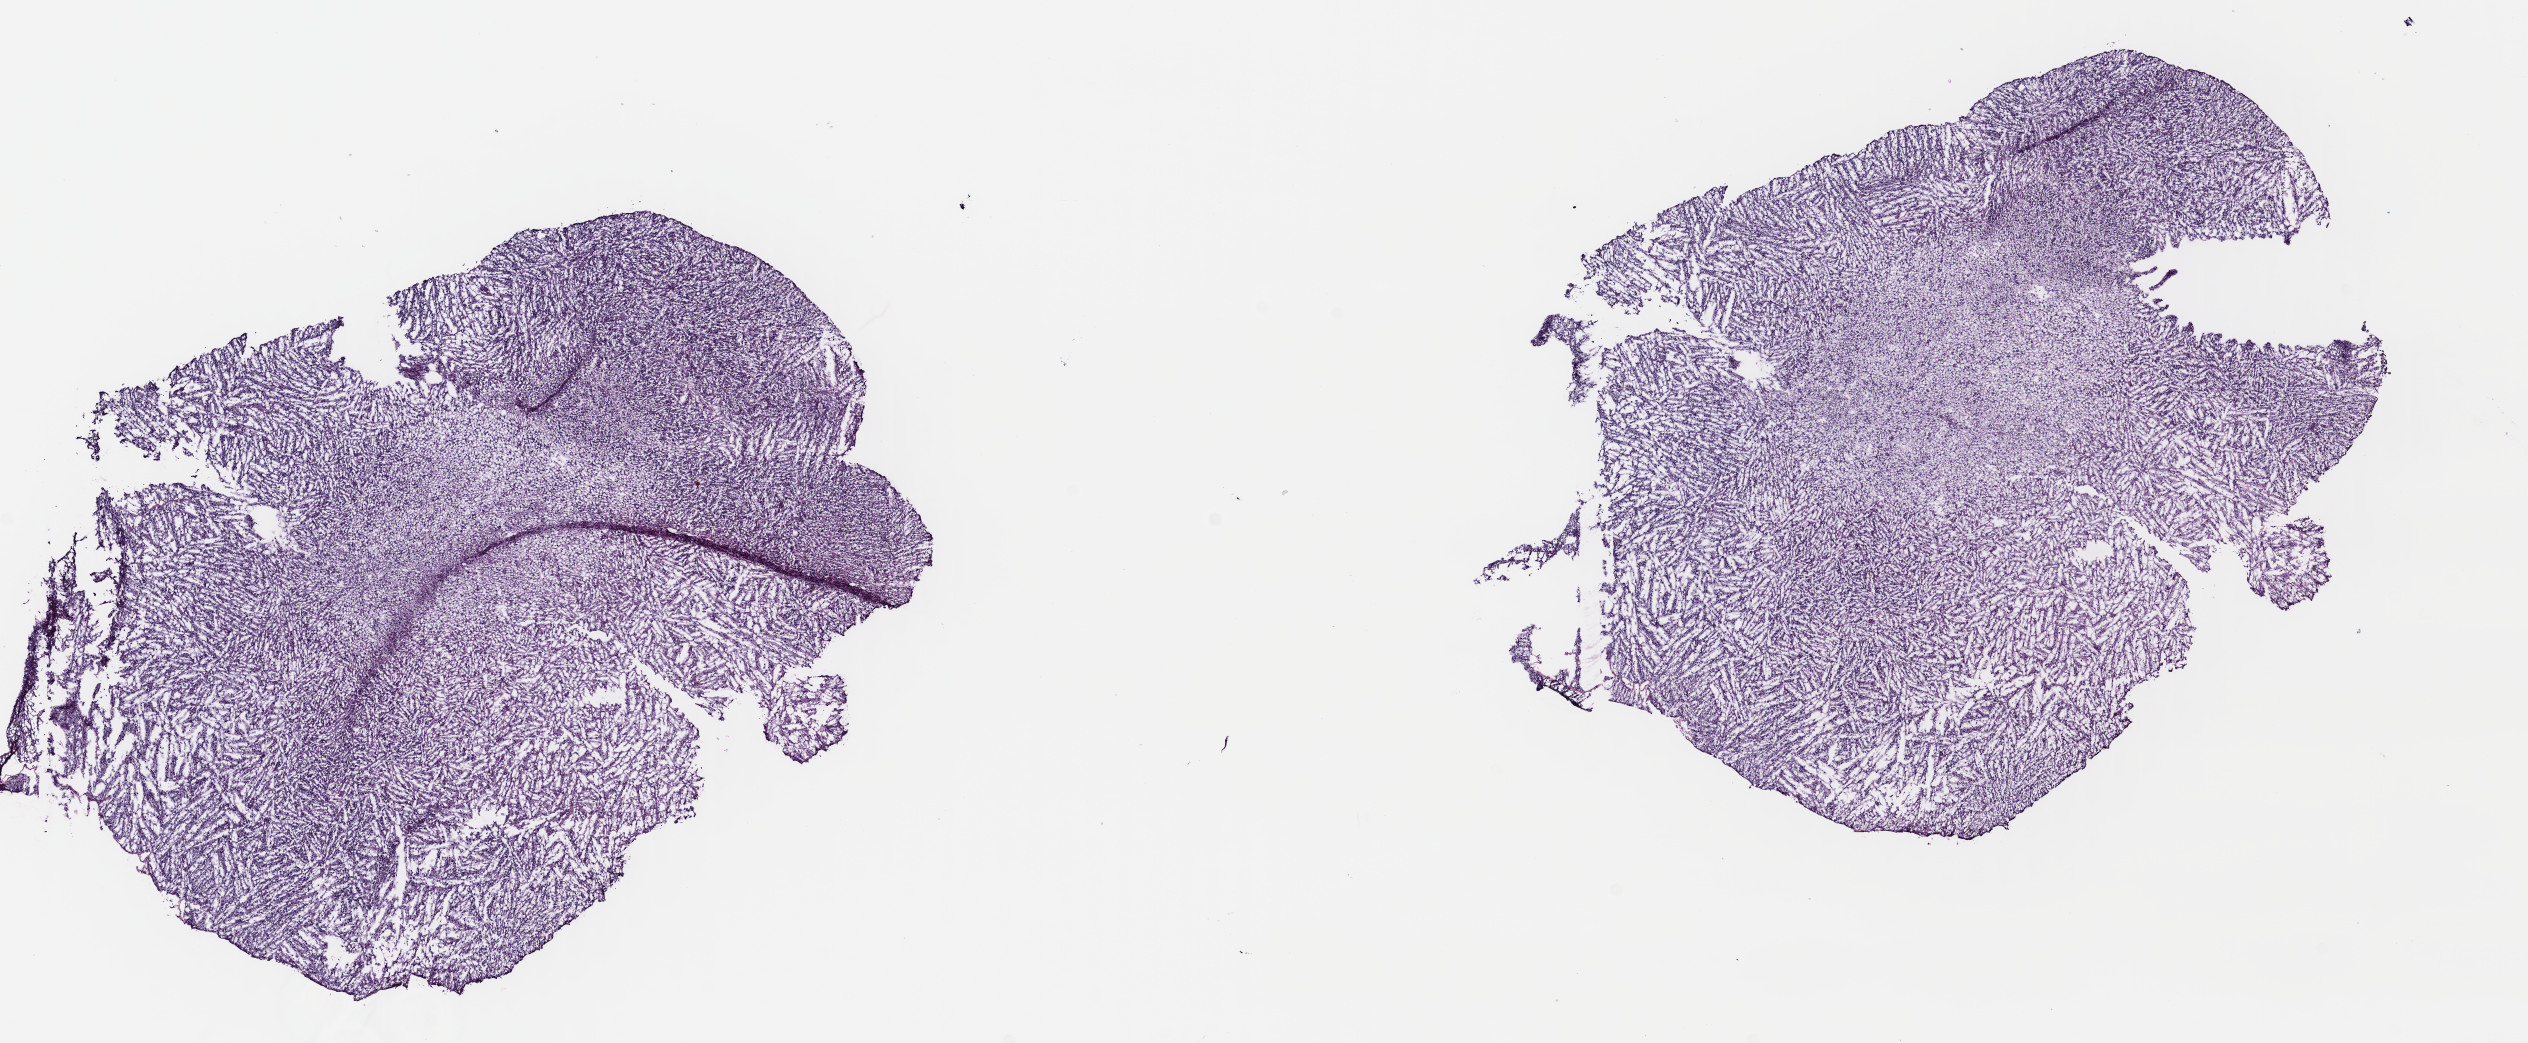
Digitized Hematoxylin and eosin (H&E) stained tissue section (whole slide) — a low-resolution overview of the entire scanned area, about 19.9 x 8.2 mm (slide scanned at 40x). Frozen section. Brain, primary tumour sample. Patient: female, age at initial diagnosis 59 years.
Pathologic diagnosis: Astrocytoma, anaplastic.